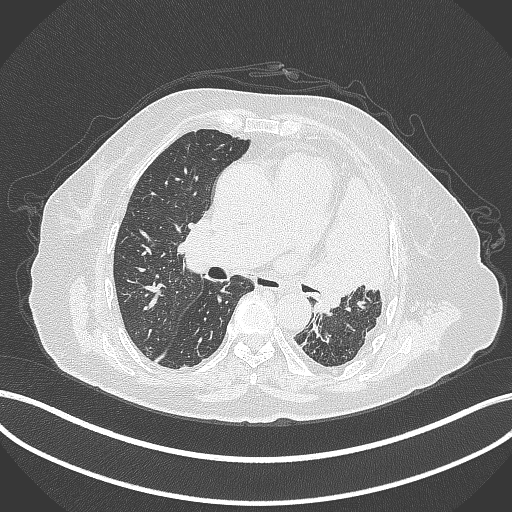
Chest CT, one axial slice. Position 211 of 399 along the scan axis. Lung window (W 1500 / L -600 HU). 1 mm slice thickness. 512 × 512 image matrix. Female patient, age 75 years. Case-level facts recorded for this patient, not image findings: clinical TNM (as recorded): T3 N3 M1.
Structures marked on this image (rectangle marked by the reading radiologist):
- lung tumour (recorded histology: adenocarcinoma): box from (x=303, y=178) to (x=392, y=320) px